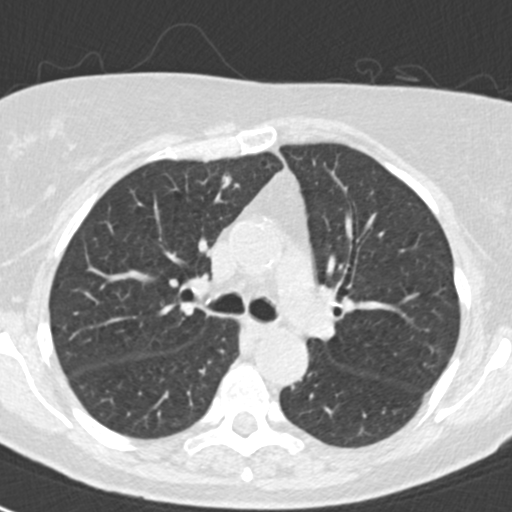
Low-dose screening chest CT, axial slice; first (baseline) screen; lung window (W 1500 / L -600 HU); standard (soft-tissue) reconstruction kernel (B30f); 120 kVp; 512 × 512 image matrix. Female participant, aged 72 years at enrolment. Former smoker at enrolment.
Expert reader's lesion annotation, box from (x=203, y=161) to (x=250, y=208) px. No non-calcified nodule or mass ≥4 mm was recorded by the screening reader at this exam. Lung cancer was diagnosed 828 days after this screen: adenocarcinoma, NOS, right upper lobe, moderately differentiated (G2), stage IA (AJCC 6th edition), 15 mm at pathology.